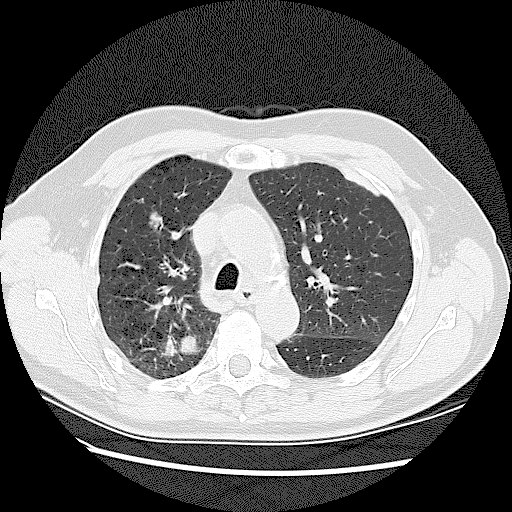
Chest CT (low-dose screening protocol), one axial image, baseline screening round, lung window (W 1500 / L -600 HU), lung (sharp) reconstruction kernel (LUNG), slice 41 of 128 in the series, 512 × 512 image matrix. Male, age 72 years at enrolment. Current smoker at enrolment.
2 lesions marked by an expert reader on this slice (largest first), bounding box (x1, y1, x2, y2) in pixels: (141, 313, 214, 378); (132, 204, 182, 243). The screening reader recorded 2 non-calcified nodules or masses ≥4 mm on this exam (right upper lobe, right upper lobe); which of them these boxes mark is not recorded.